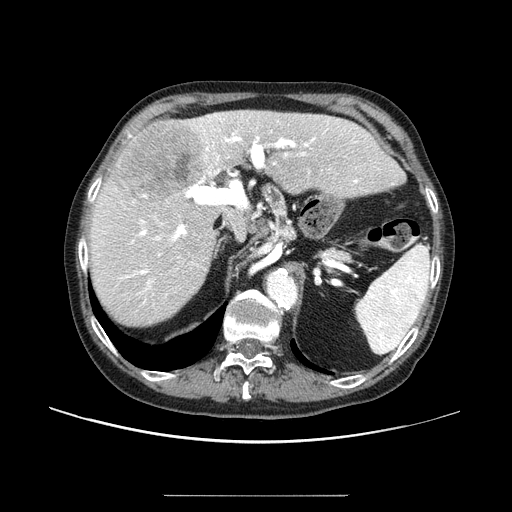
Contrast-enhanced abdominal CT (liver protocol), one axial slice. Slice 60 of 91 in the series (ordered by position). One of 2 acquisitions stored at this slice position. Soft-tissue window (W 400 / L 40 HU). 2.5 mm slice thickness. 512 × 512 image matrix, field of view 400 × 400 mm. Case-level facts recorded for this patient, not image findings: diagnosis: hepatocellular carcinoma (patient treated with transarterial chemoembolisation; whether this scan precedes or follows treatment is not stated here); TNM stage (as recorded): Stage-I; Child-Pugh class: A; tumour nodularity: uninodular.
Annotated regions visible in this slice (semi-automatically segmented with operator editing):
- liver parenchyma outside the tumour (the mass and vessels are separate outlines, so this box may not span the whole liver): bounding box (x1, y1, x2, y2) in pixels: (90, 110, 378, 326)
- mass: (111, 121, 203, 203)
- liver vessels: (98, 113, 358, 304)